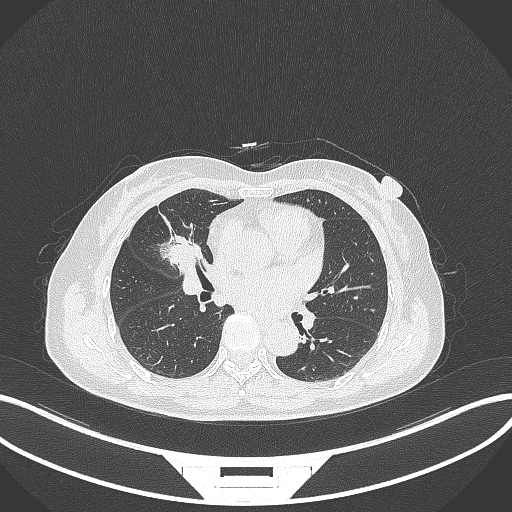
Chest CT, one axial slice. Position 153 of 284 along the scan axis. Reconstruction kernel B70f. Lung window (W 1500 / L -600 HU). 1 mm slice thickness. 512 × 512 image matrix, field of view 400 × 400 mm. Female patient, age 51 years. From the clinical record (not read from this slice): clinical TNM (as recorded): T1c N0 M0; histopathological grade: G2.
Structures marked on this image (bounding box drawn by a radiologist):
- lung tumour (recorded histology: adenocarcinoma): bounding box (x1, y1, x2, y2) in pixels: (158, 229, 203, 272)